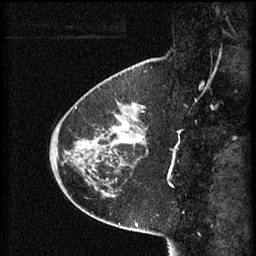
Breast MRI (dynamic contrast-enhanced), one sagittal slice. Position 19 of 60 along the scan axis. 3 images stored at this slice position (order not interpretable as contrast timing). 1.5 T. TE 4.2 ms, TR 8.2 ms. 2 mm slice thickness. 256 × 256 image matrix, field of view 200 × 200 mm. Female patient, age 45 years.
Annotated regions visible in this slice (semi-automatic segmentation, software-assisted and operator-edited):
- analysis volume of interest (the breast-tissue region the enhancement analysis was run in; not a lesion): bounding box [x1, y1, x2, y2] px = [80, 102, 148, 171]
- tumour enhancement mask (voxels above the 70 % enhancement threshold inside the analysis volume of interest): [85, 128, 127, 145]